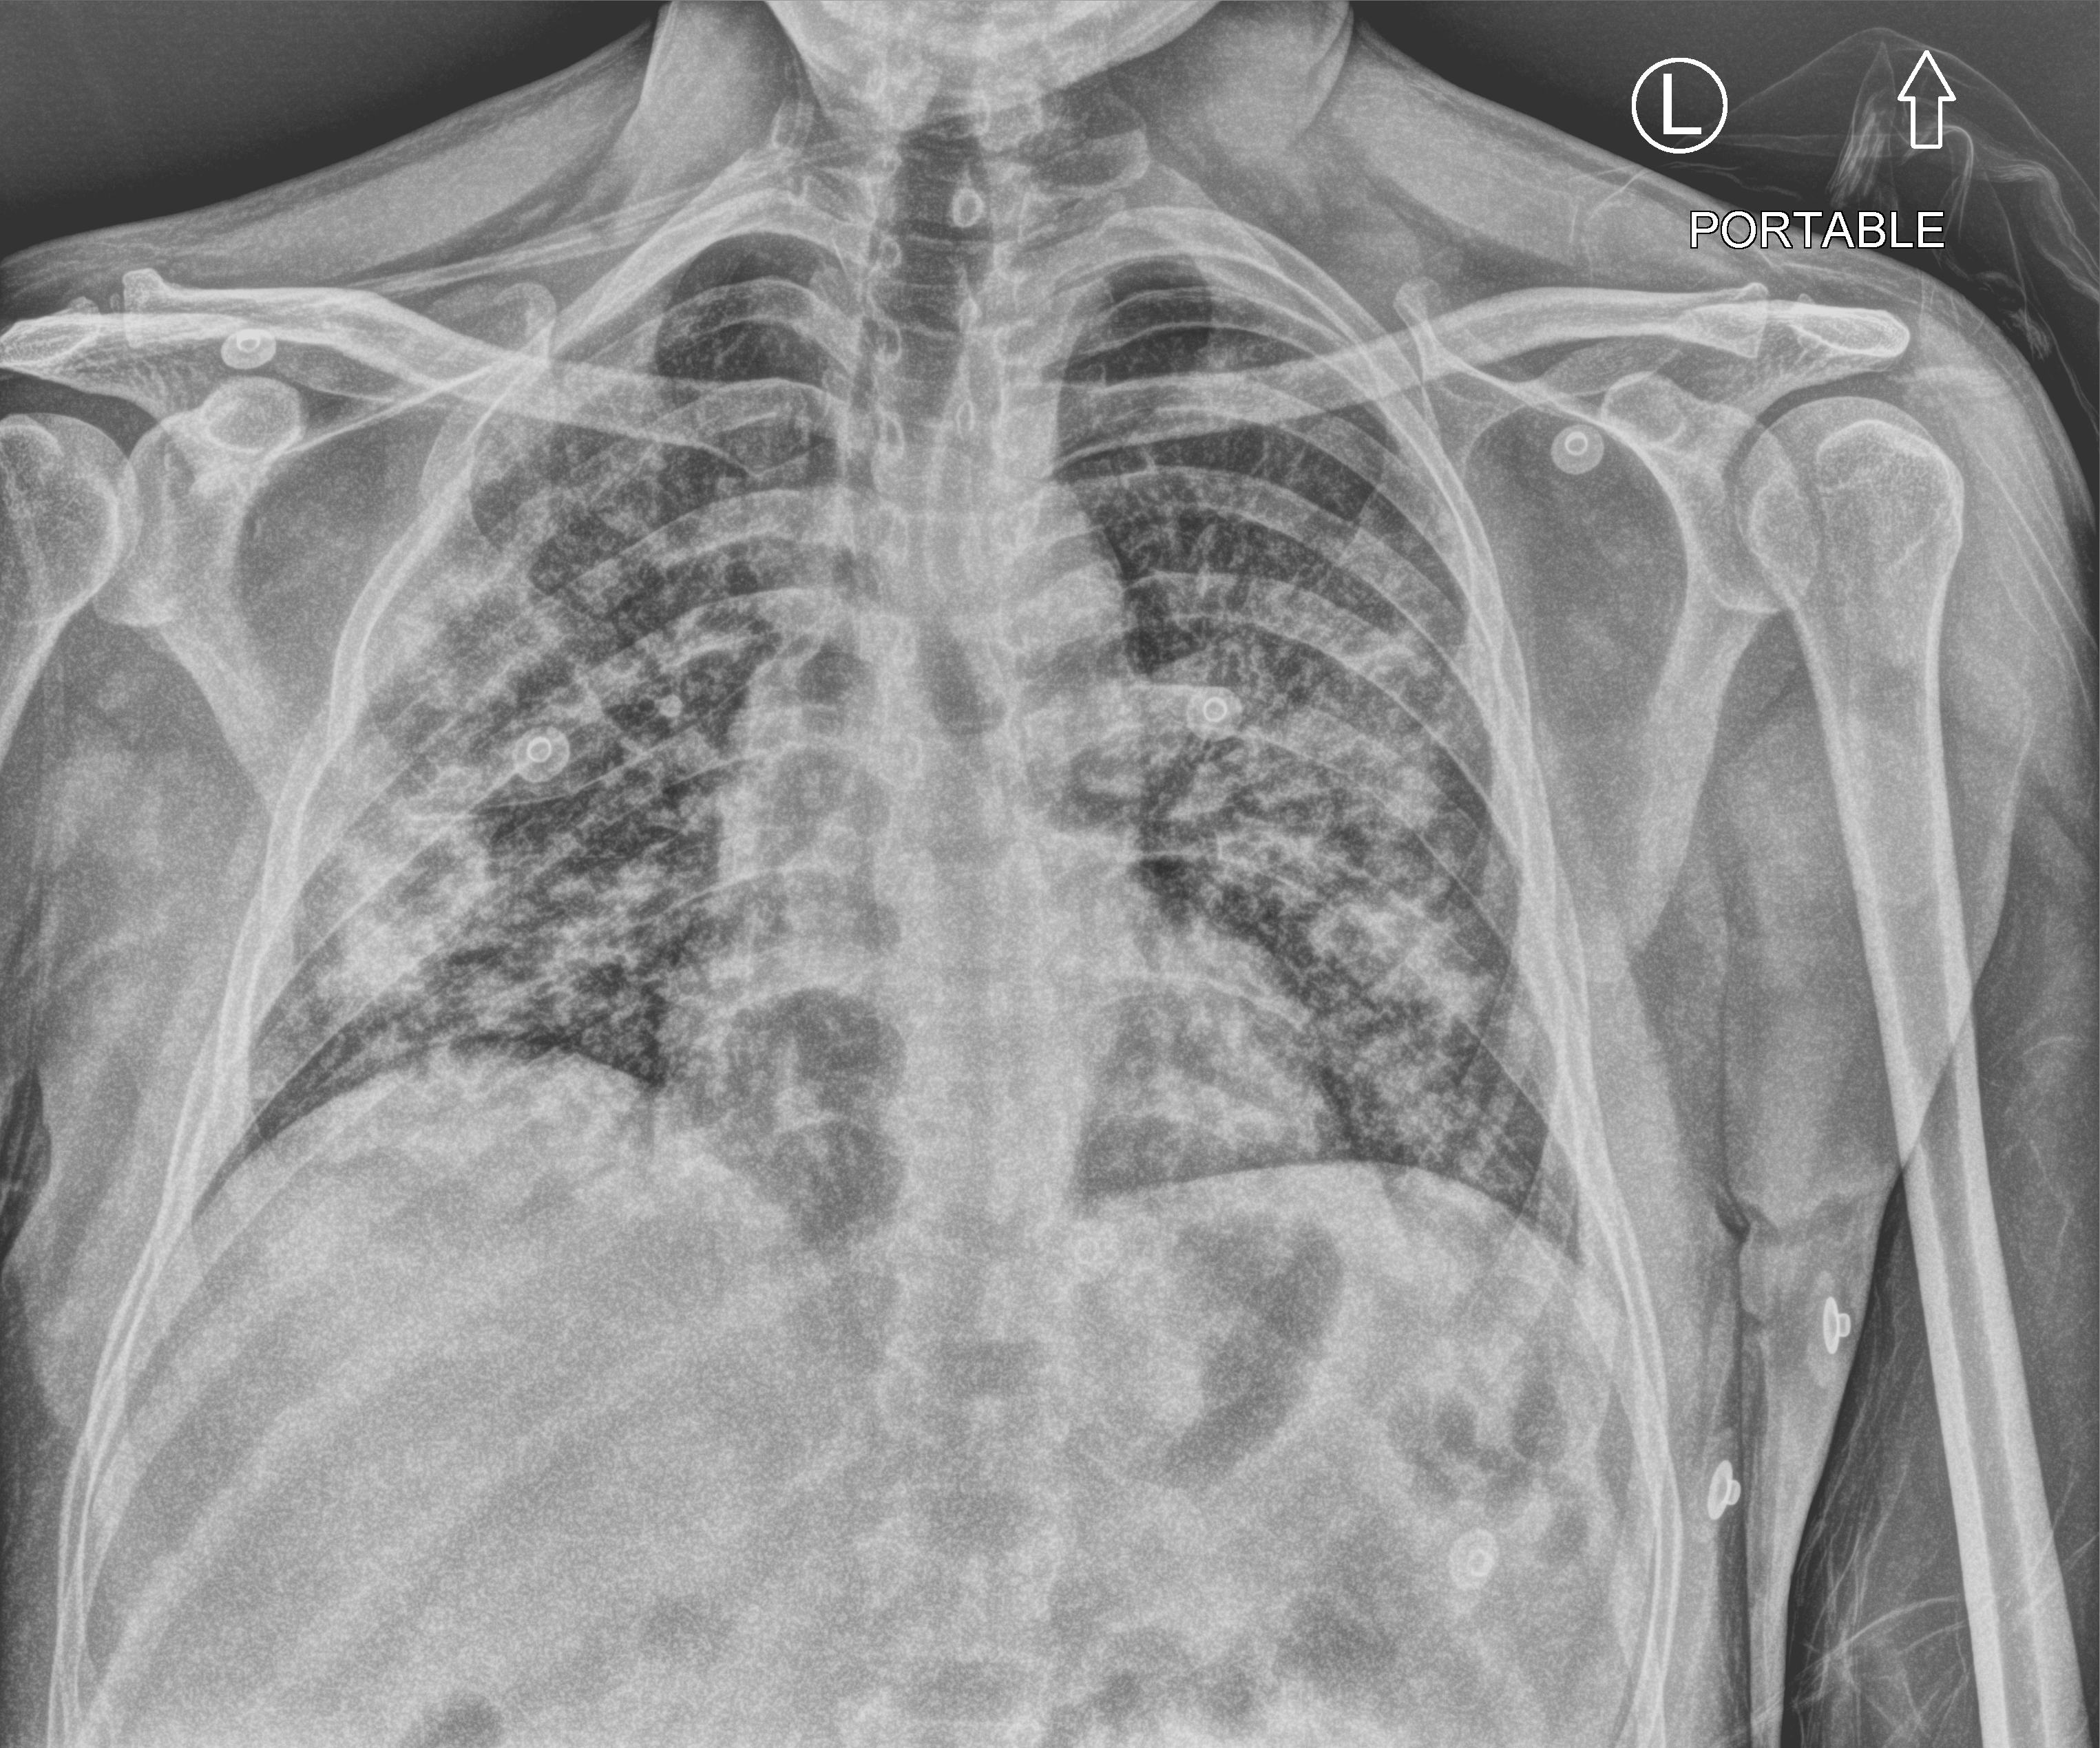
Bedside chest radiograph (computed radiography); anteroposterior (AP) projection. Patient hospitalised with COVID-19, aged 18–59 years.
From the hospital-stay record, not from the radiograph (when in the stay this image was taken is not recorded):
- hypertension (admission record): no
- mechanically ventilated during this hospital stay: yes